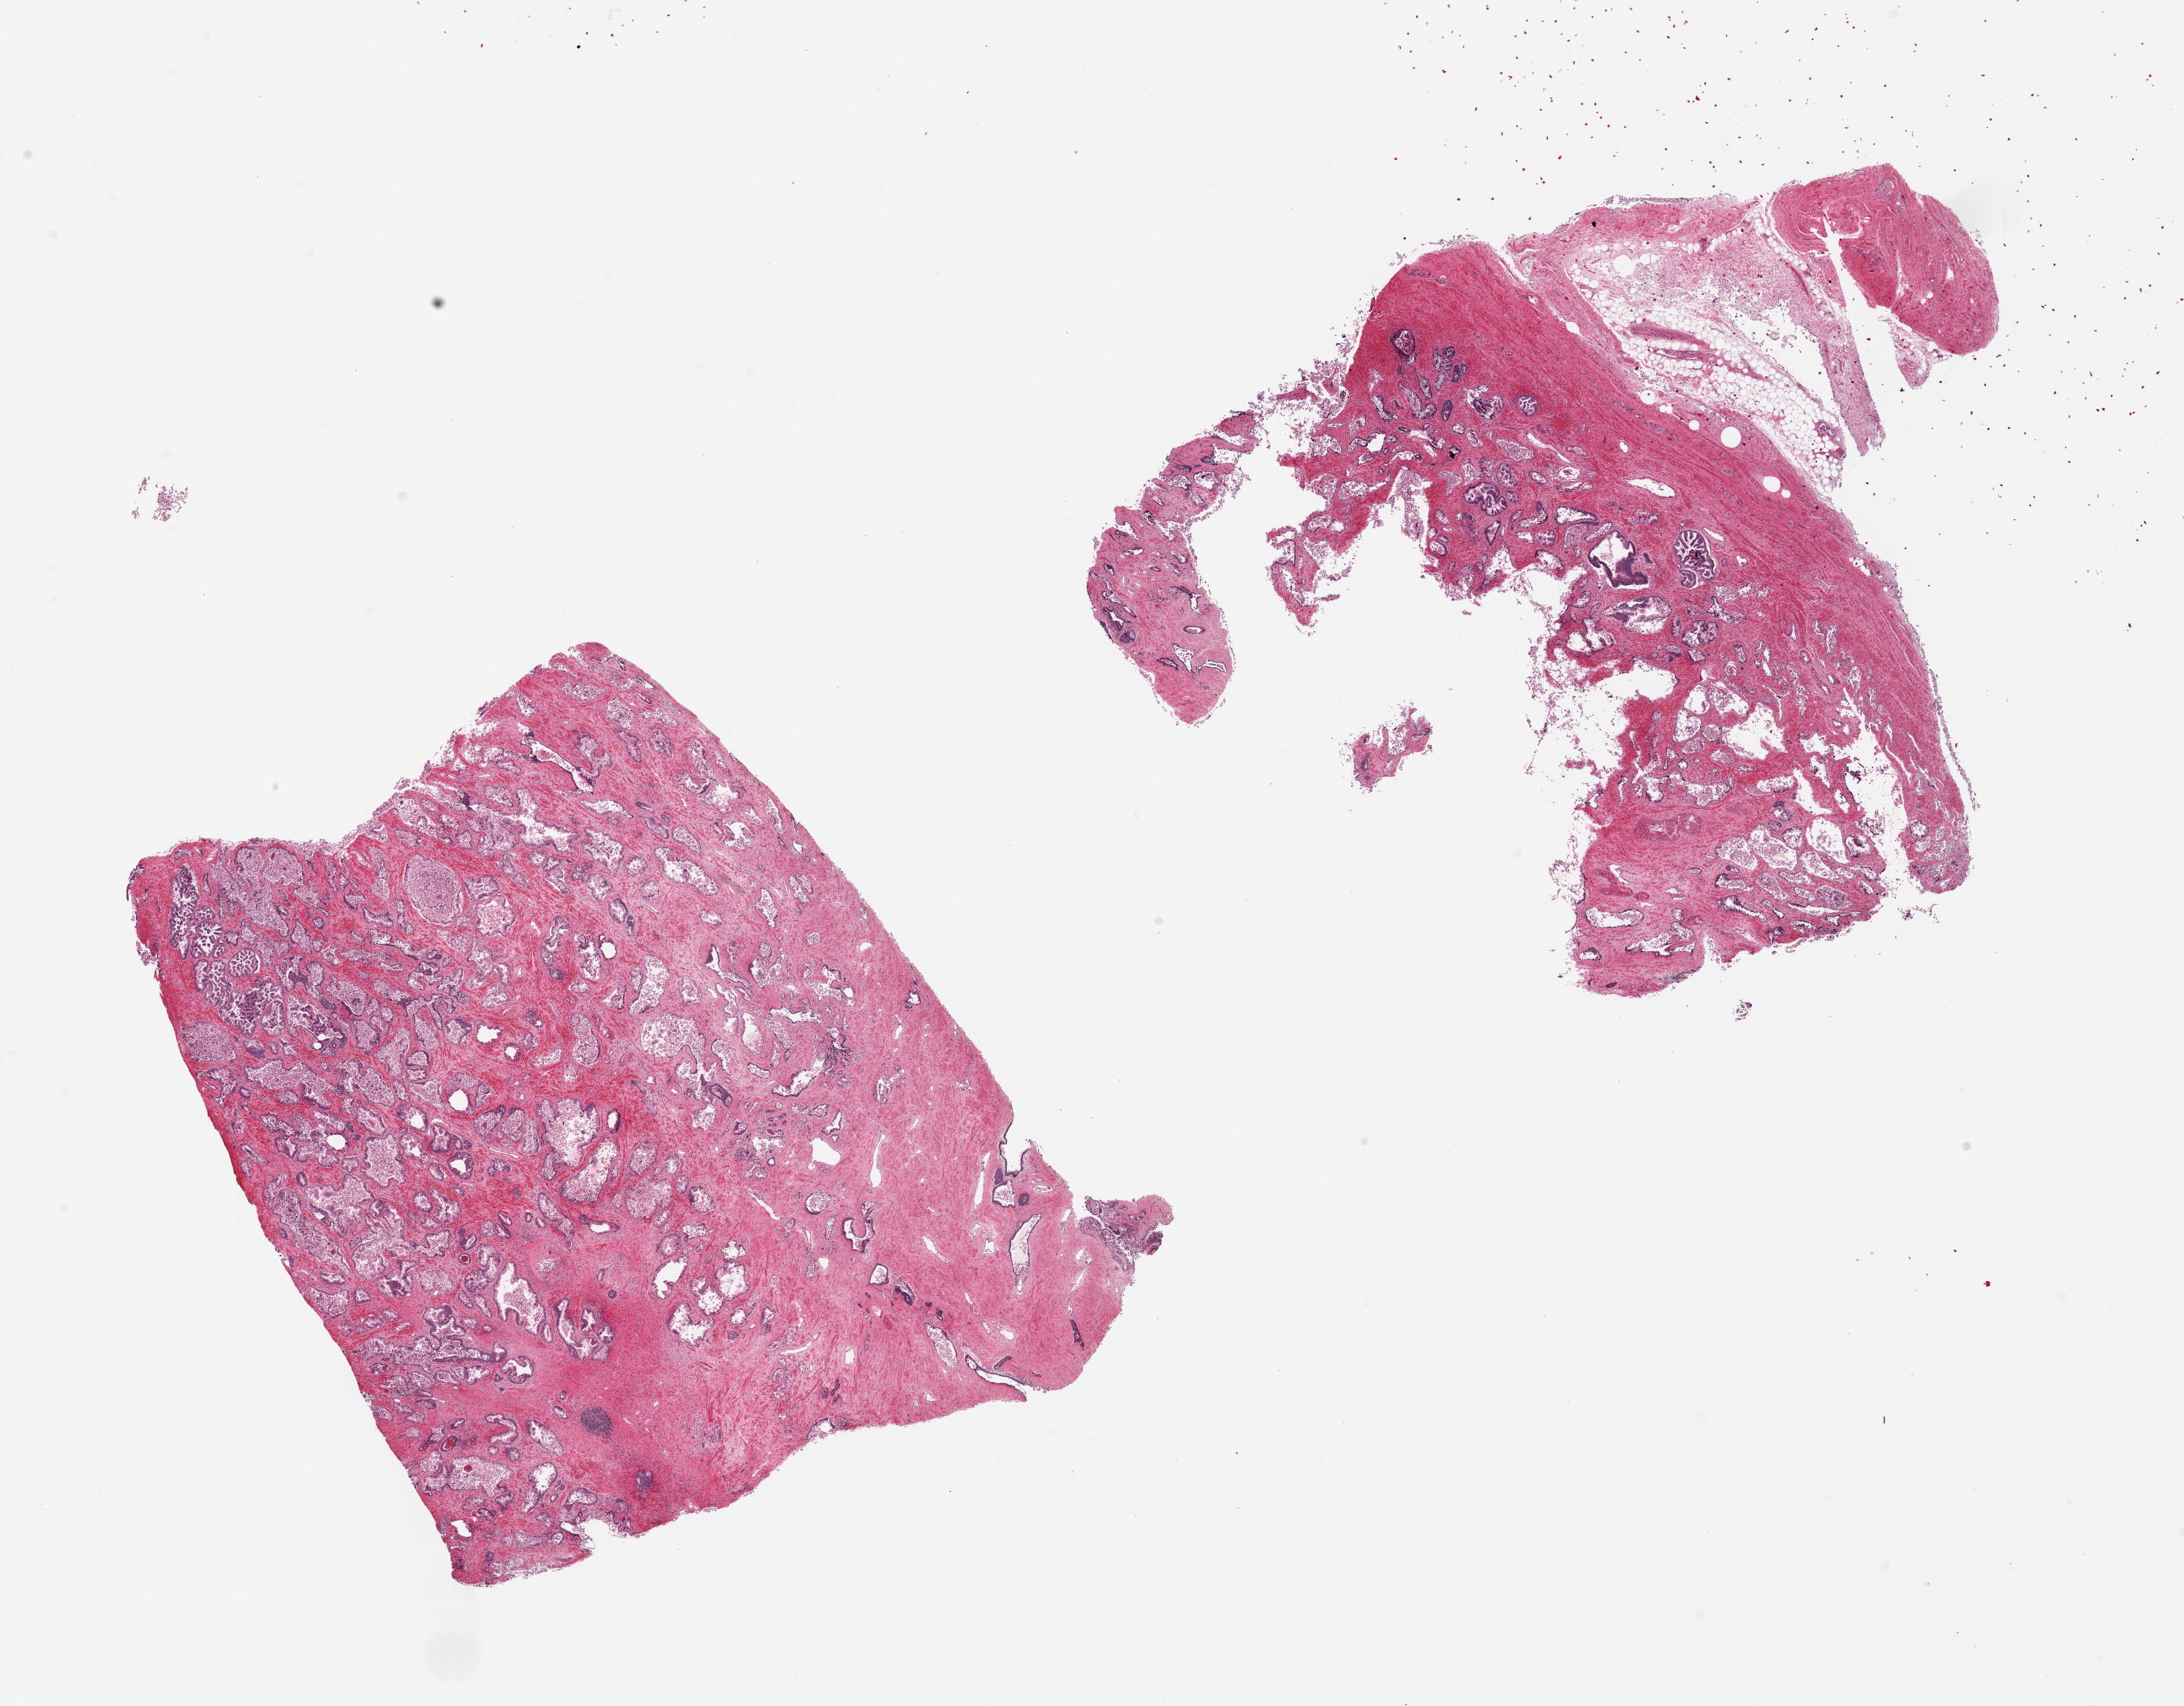
Whole-slide image, haematoxylin and eosin stain, brightfield — a low-resolution overview of the entire scanned area, about 23.6 x 18.5 mm (slide scanned at 20x); PAXgene-fixed paraffin-embedded (PFPE) section; sampled site (target tissue): prostate; tissue donor sample. Donor: male.
Reviewer comment on this tissue sample: 2 pieces, 9.5x9 and 9x8mm; moderate glandular autolysis; one has nubbine of adherent fat/stroma.